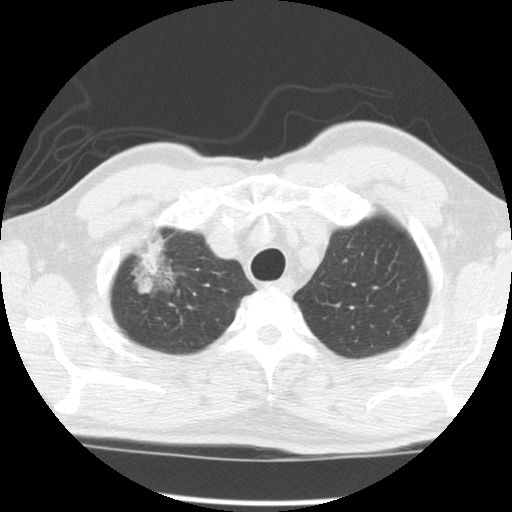
Low-dose screening chest CT, axial slice; second screening round (one year after baseline); lung window (W 1500 / L -600 HU); 2.5 mm slice thickness; standard (soft-tissue) reconstruction kernel (STANDARD); slice 17 of 120 in the series. Male participant, aged 64 years at enrolment. Former smoker at enrolment.
Lesion marked by an expert reader, bounding box (x1, y1, x2, y2) in pixels: (122, 235, 190, 304). The screening reader recorded 2 non-calcified nodules or masses ≥4 mm on this exam (right upper lobe, left upper lobe); which of them this box marks is not recorded. Official screen result: positive, other. Later outcome: lung cancer diagnosed 429 days after this screen — adenocarcinoma, NOS, right upper lobe, well differentiated (G1), stage IB (AJCC 6th edition), 45 mm at pathology.